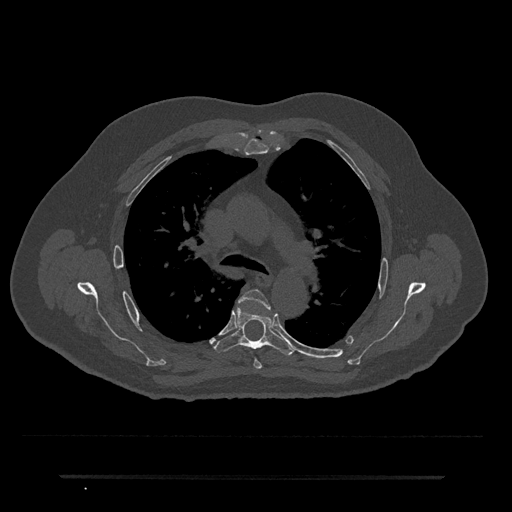
CT including the spine, one axial slice. Slice 496 of 797 in the series (ordered by position). Reconstruction kernel Br40s/3. Bone window (W 1800 / L 400 HU). 512 × 512 image matrix. Male patient, age 69 years. From the clinical record (not read from this slice): primary cancer: prostate.
Structures marked on this image (semi-automatically segmented with operator editing):
- T4 vertebra: box from (x=239, y=289) to (x=270, y=369) px
- T5 vertebra: (x=214, y=307)–(x=295, y=355)